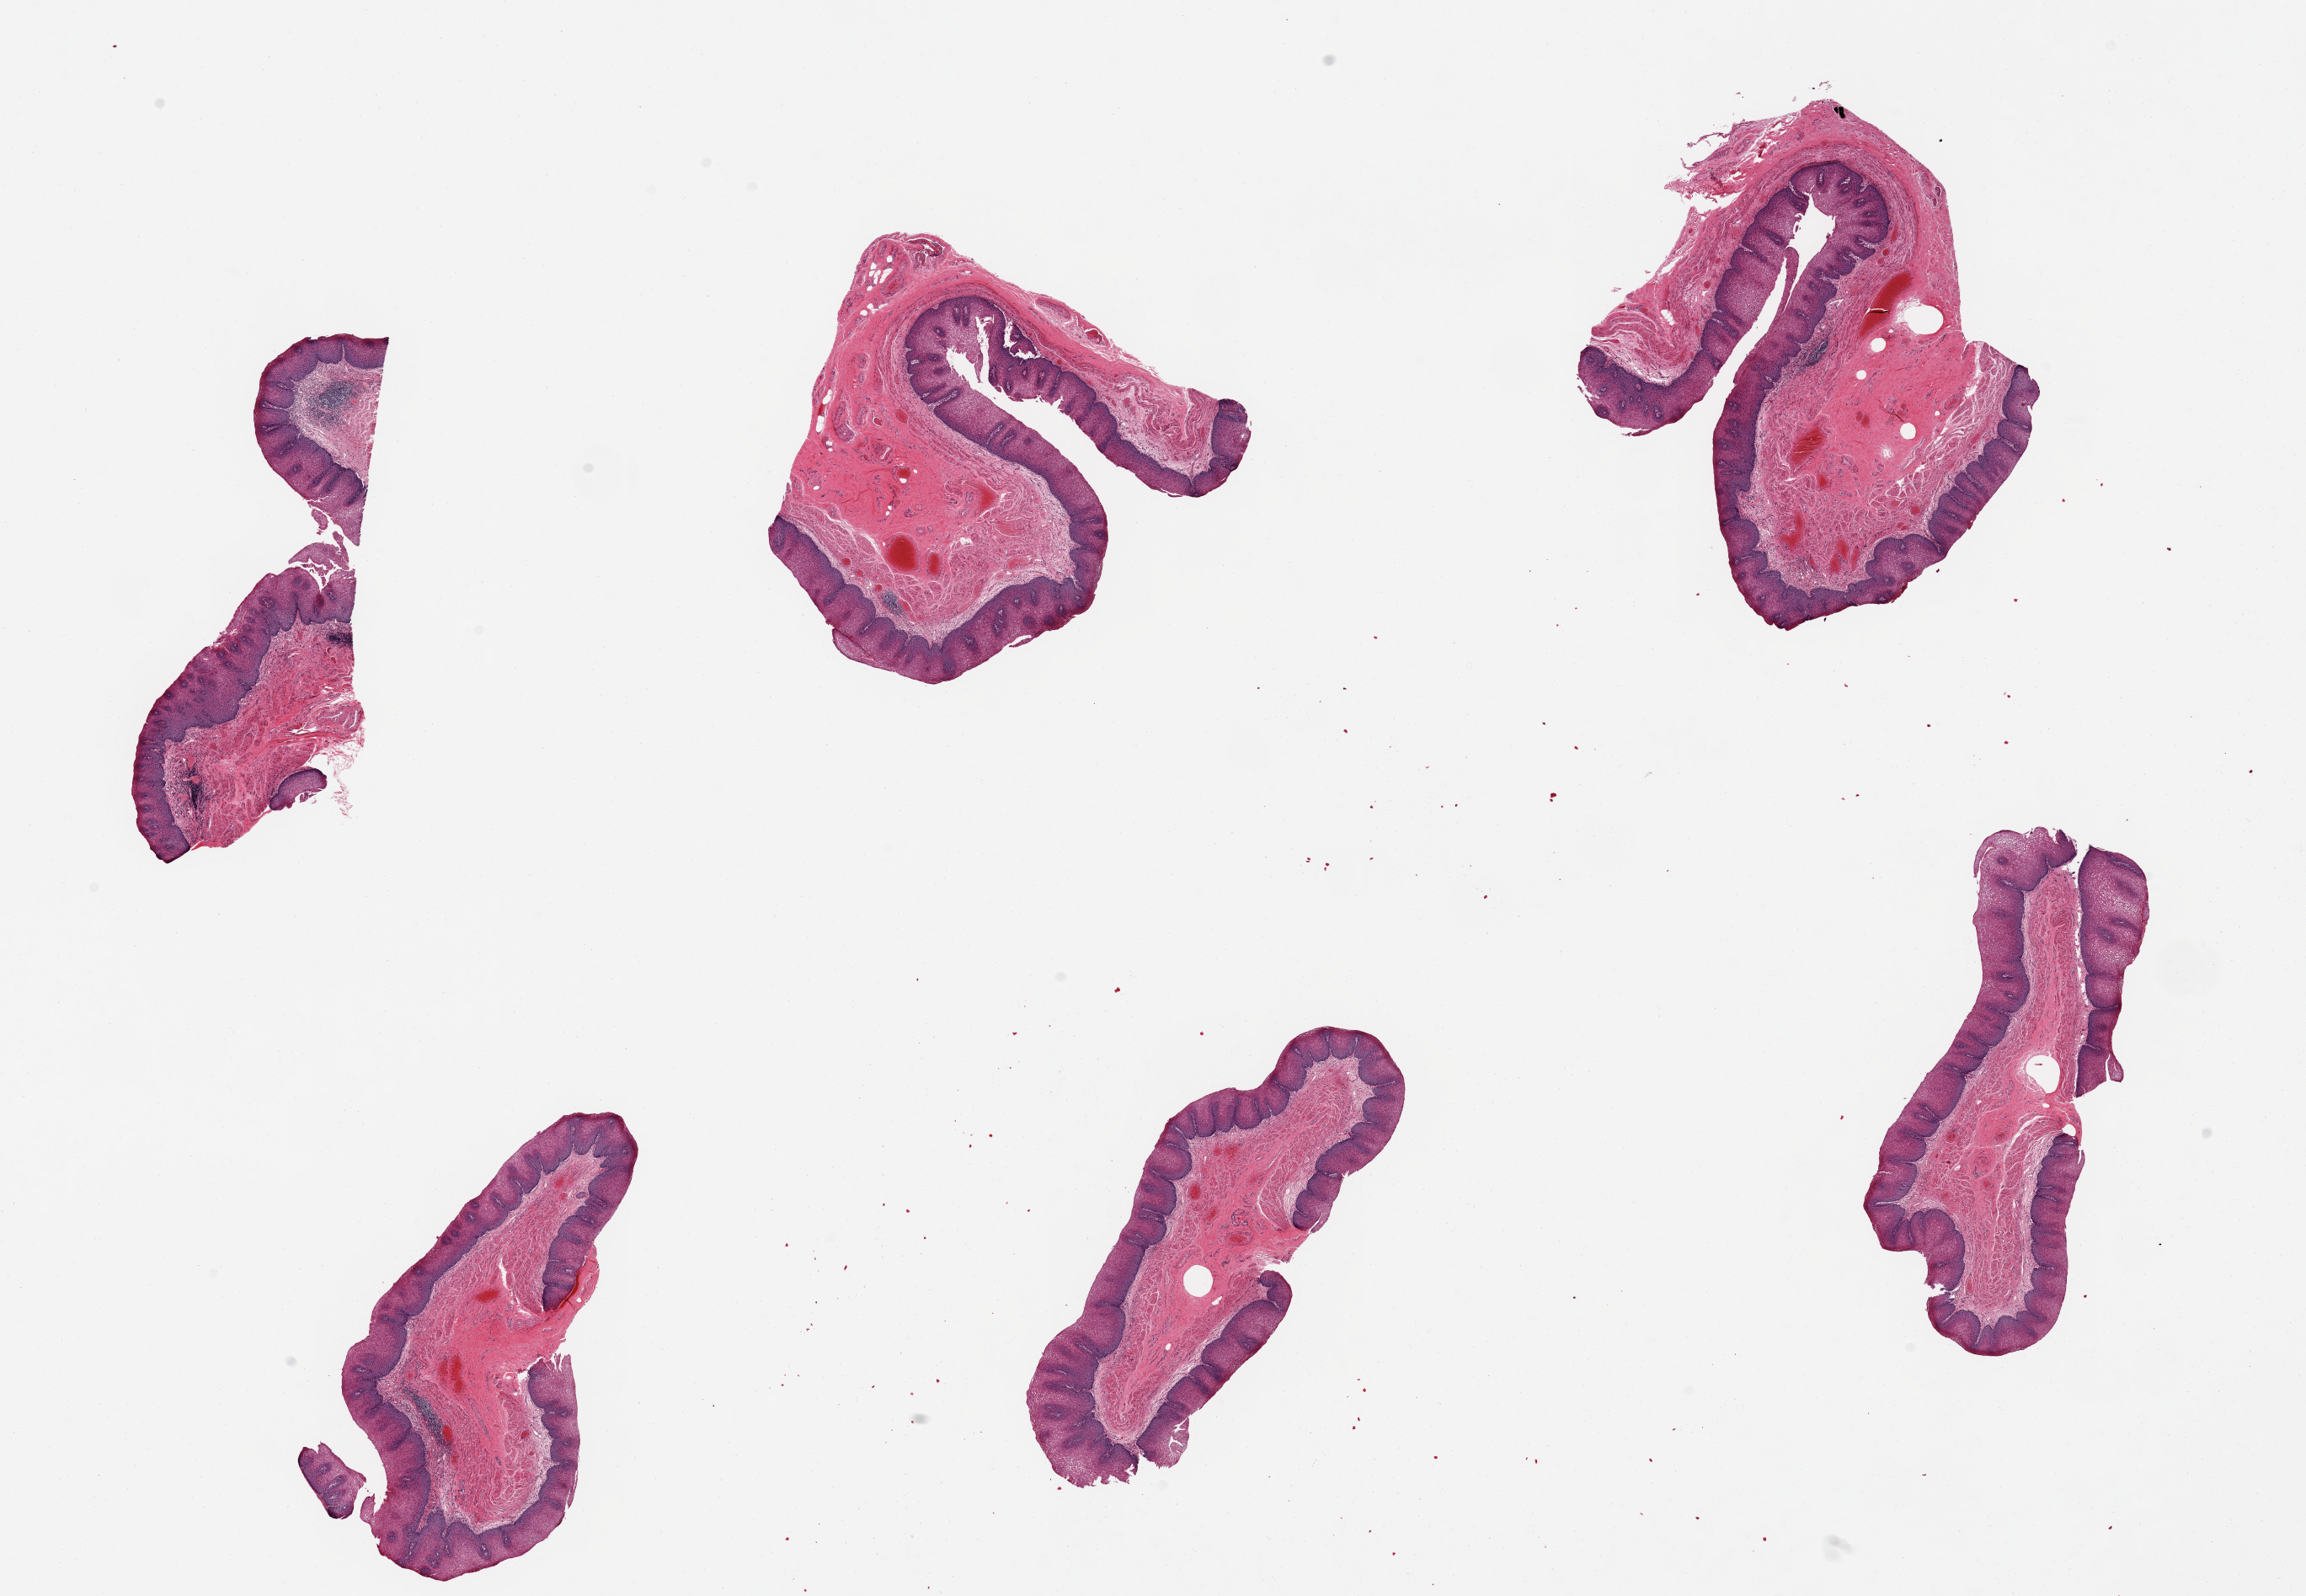
Whole-slide image, hematoxylin and eosin (H&E) stain, brightfield, low-resolution overview of the scanned area, about 21.7 x 15.0 mm (from a 20x scan), PAXgene-fixed paraffin-embedded (PFPE) section, sampled site (target tissue): esophageal mucous membrane, tissue donor sample. Male donor.
• pathologist's review note for this sample: 6 pieces